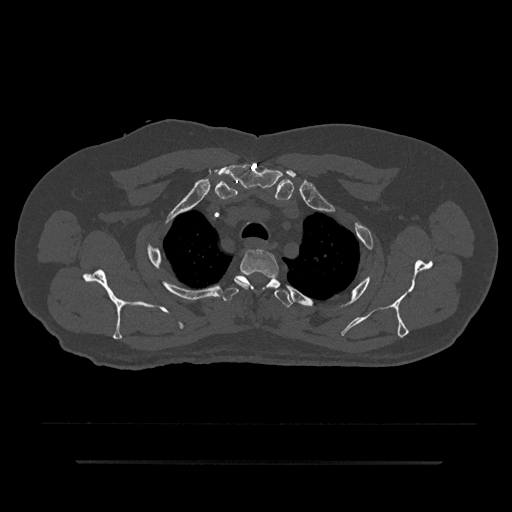
CT including the spine, one axial slice. Slice 680 of 797 in the series (ordered by position). Bone window (W 1800 / L 400 HU). 512 × 512 image matrix, field of view 464 × 464 mm. Patient: male, 59 years. Case-level facts recorded for this patient, not image findings: primary cancer: bile ducts; vertebrae with lytic lesions (as recorded): T10.
Annotated regions visible in this slice (semi-automatic segmentation, software-assisted and operator-edited):
- T2 vertebra: bounding box (x1, y1, x2, y2) in pixels: (234, 249, 279, 291)
- T3 vertebra: (222, 275, 293, 307)